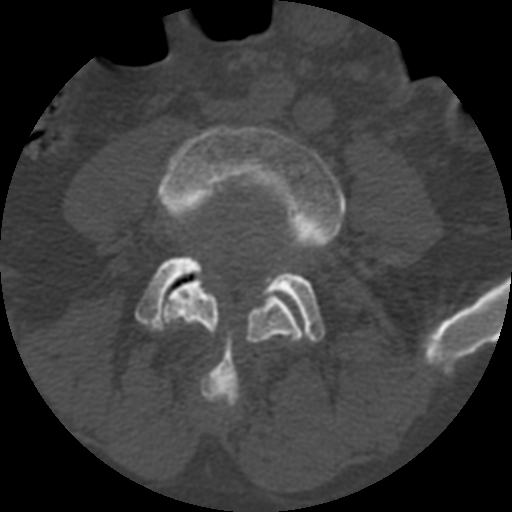
CT including the spine, one axial slice. Position 270 of 399 along the scan axis. Reconstruction kernel STANDARD. Bone window (W 1800 / L 400 HU). 1.25 mm slice thickness. 512 × 512 image matrix, field of view 160 × 160 mm. Patient age 71 years. From the clinical record (not read from this slice): primary cancer: prostate.
Outlined on this slice (semi-automatic segmentation, software-assisted and operator-edited):
- L4 vertebra: box from (x=157, y=126) to (x=345, y=410) px
- L5 vertebra: (x=136, y=255)–(x=325, y=342)